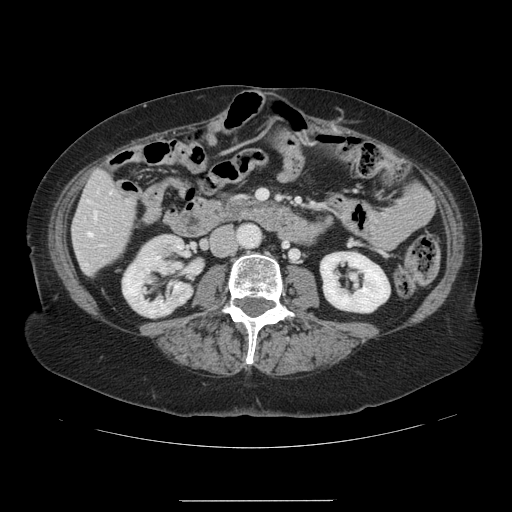
Contrast-enhanced abdominal CT, one axial slice; position 31 of 141 along the scan axis; intravenous contrast given; soft-tissue window (W 400 / L 40 HU); 2.5 mm slice thickness; 512 × 512 image matrix, field of view 393 × 393 mm. Female patient, age 74 years. From the clinical record (not read from this slice): diagnosis: colorectal cancer liver metastases, imaged before liver resection; multiple liver metastases: yes; largest metastasis: 7 cm.
Outlined on this slice (outlined manually by an expert reader):
- hepatic veins: bounding box [x1, y1, x2, y2] px = [88, 215, 96, 236]
- liver: [73, 173, 135, 273]
- planned liver remnant (the part of the liver to remain after resection): [77, 196, 123, 273]